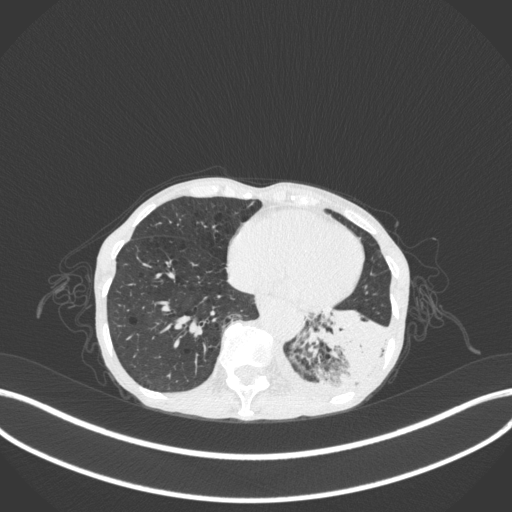
Chest CT, one axial slice; slice 62 of 347 in the series (ordered by position); reconstruction kernel B31f; 120 kVp; lung window (W 1500 / L -600 HU); 1 mm slice thickness; 512 × 512 image matrix. Female patient, age 70 years. Case-level facts recorded for this patient, not image findings: clinical TNM (as recorded): T3 N0 M0; histopathological grade: G3.
Structures marked on this image (bounding box drawn by a radiologist):
- lung tumour (recorded histology: small cell carcinoma): bounding box [x1, y1, x2, y2] px = [305, 299, 387, 396]